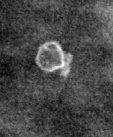
Cropped region of a digitized screen-film mammogram centred on a radiologist-marked abnormality; right breast; CC view; BI-RADS breast density category 1 (scale 1–4).
Marked abnormality: calcifications, morphology lucent centered; BI-RADS assessment category 2; subtlety rating 3 on a 1 (subtle) to 5 (obvious) scale; benign; no additional work-up was recommended (benign without callback).